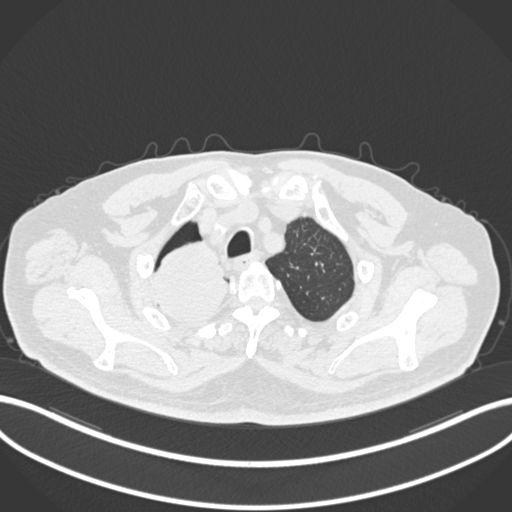
Chest CT, one axial slice; slice 184 of 218 in the series (ordered by position); 120 kVp; lung window (W 1500 / L -600 HU); 1 mm slice thickness; 512 × 512 image matrix, field of view 400 × 400 mm. Male patient, age 68 years. From the clinical record (not read from this slice): clinical TNM (as recorded): T2a N0 M0.
Outlined on this slice (bounding box drawn by a radiologist):
- lung tumour (recorded histology: adenocarcinoma): bounding box [x1, y1, x2, y2] px = [150, 240, 235, 327]